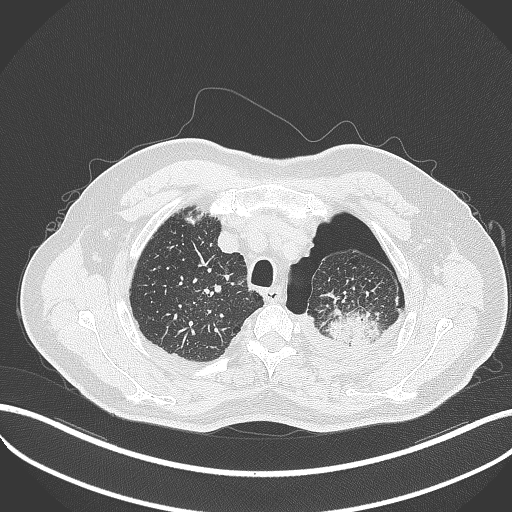
Chest CT, one axial slice. Position 414 of 464 along the scan axis. Reconstruction kernel B70f. Lung window (W 1500 / L -600 HU). 1 mm slice thickness. 512 × 512 image matrix, field of view 400 × 400 mm. Male patient, age 76 years. From the clinical record (not read from this slice): clinical TNM (as recorded): T3 N0 M1b.
Outlined on this slice (rectangle marked by the reading radiologist):
- lung tumour (recorded histology: adenocarcinoma): bounding box [x1, y1, x2, y2] px = [327, 306, 381, 350]